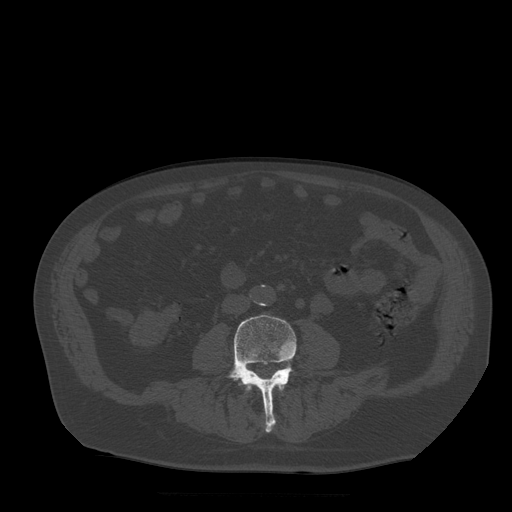
CT including the spine, one axial slice; bone window (W 1800 / L 400 HU); 1.25 mm slice thickness; 512 × 512 image matrix. Patient age 72 years. From the clinical record (not read from this slice): primary cancer: prostate.
Outlined on this slice (semi-automatic segmentation, software-assisted and operator-edited):
- L3 vertebra: bounding box <245,383,284,393> (left, top, right, bottom; pixels)
- L4 vertebra: <225,315,297,433>
- L5 vertebra: <243,359,294,385>